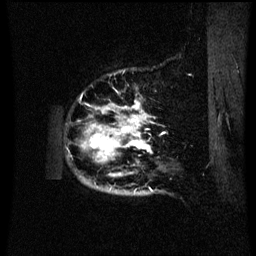
Breast MRI (dynamic contrast-enhanced), one sagittal slice. Dynamic contrast-enhanced series, image 2 of 3 at this slice position (ordered by acquisition). 1.5 T. TE 4.2 ms, TR 8.9 ms. 2.1 mm slice thickness. 256 × 256 image matrix, field of view 200 × 200 mm. Female patient, age 42 years. From the clinical record (not read from this slice): setting: breast cancer imaged before/during neoadjuvant chemotherapy; receptor status: HER2-positive.
Annotated regions visible in this slice (semi-automatically segmented with operator editing):
- analysis volume of interest (the breast-tissue region the enhancement analysis was run in; not a lesion): bounding box [x1, y1, x2, y2] px = [72, 88, 169, 193]
- tumour enhancement mask (voxels above the 70 % enhancement threshold inside the analysis volume of interest): [84, 102, 151, 177]